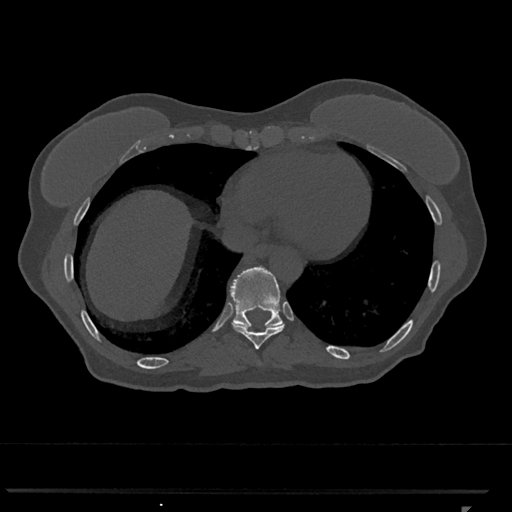
CT including the spine, one axial slice; slice 599 of 793 in the series (ordered by position); bone window (W 1800 / L 400 HU); 0.5 mm slice thickness; 512 × 512 image matrix. Female patient, age 62 years. Case-level facts recorded for this patient, not image findings: primary cancer: renal.
Annotated regions visible in this slice (semi-automatic segmentation, software-assisted and operator-edited):
- T10 vertebra: bounding box (x1, y1, x2, y2) in pixels: (230, 266, 283, 327)
- T9 vertebra: (232, 306, 285, 349)